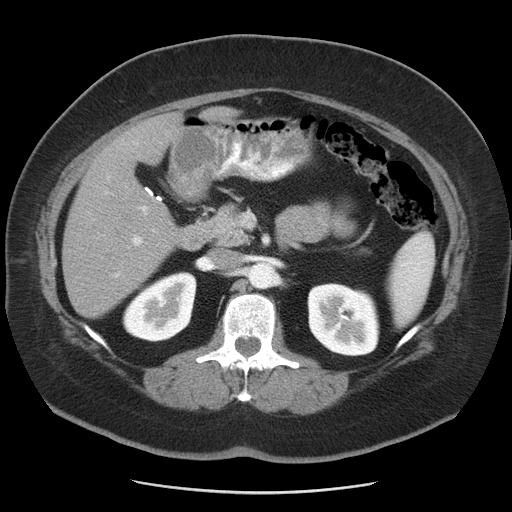
Contrast-enhanced abdominal CT, one axial slice; position 23 of 55 along the scan axis; 120 kVp; intravenous contrast given; soft-tissue window (W 400 / L 40 HU); 5 mm slice thickness; 512 × 512 image matrix, field of view 380 × 380 mm. Female patient, age 52 years. From the clinical record (not read from this slice): diagnosis: colorectal cancer liver metastases, imaged before liver resection; multiple liver metastases: yes; largest metastasis: 2.5 cm; disease in both lobes: yes.
Structures marked on this image (manually delineated by an expert):
- liver: bounding box [x1, y1, x2, y2] px = [62, 113, 182, 318]
- planned liver remnant (the part of the liver to remain after resection): [62, 192, 180, 318]
- portal vein (with intrahepatic branches): [102, 140, 157, 277]